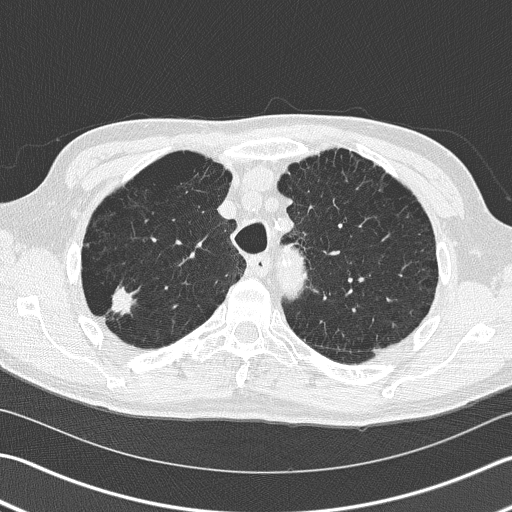
Low-dose screening chest CT, one axial slice. Position 123 of 163 along the scan axis. Lung window (W 1500 / L -600 HU). 512 × 512 image matrix, field of view 346 × 346 mm.
Structures marked on this image (manually delineated by an expert):
- lesion 1 (tumor, upper lobe of right lung): bounding box [x1, y1, x2, y2] px = [111, 288, 132, 315]